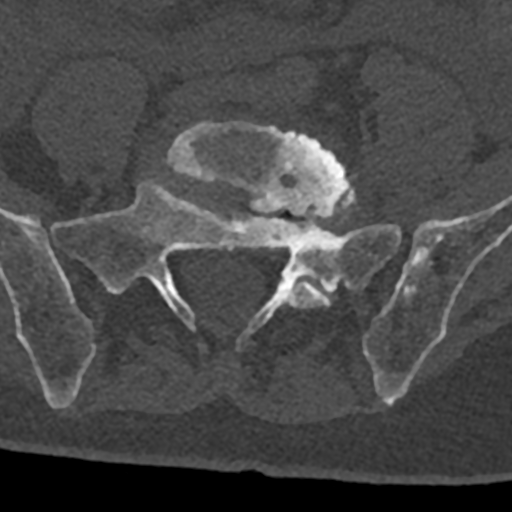
CT including the spine, one axial slice; slice 168 of 797 in the series (ordered by position); reconstruction kernel Br40s/3; bone window (W 1800 / L 400 HU); 512 × 512 image matrix, field of view 160 × 160 mm. Patient: male, 74 years. Case-level facts recorded for this patient, not image findings: primary cancer: renal.
Structures marked on this image (semi-automatic segmentation, software-assisted and operator-edited):
- L5 vertebra: bounding box [x1, y1, x2, y2] px = [167, 122, 356, 309]